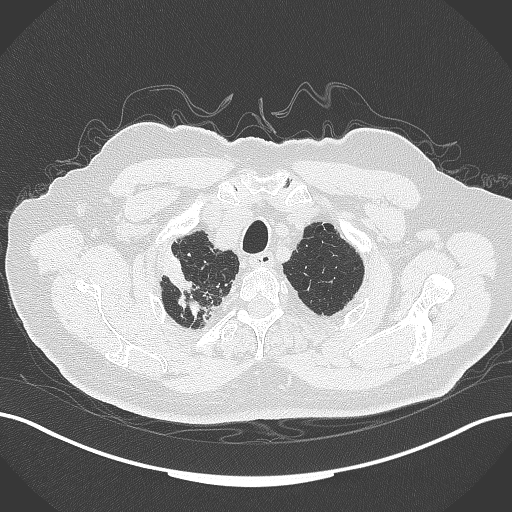
Chest CT, one axial slice; position 321 of 389 along the scan axis; lung window (W 1500 / L -600 HU); 1 mm slice thickness; 512 × 512 image matrix, field of view 400 × 400 mm. Male patient, age 72 years. Case-level facts recorded for this patient, not image findings: clinical TNM (as recorded): T1a N0 M0.
Structures marked on this image (rectangle marked by the reading radiologist):
- lung tumour (recorded histology: squamous cell carcinoma): box from (x=162, y=250) to (x=200, y=293) px